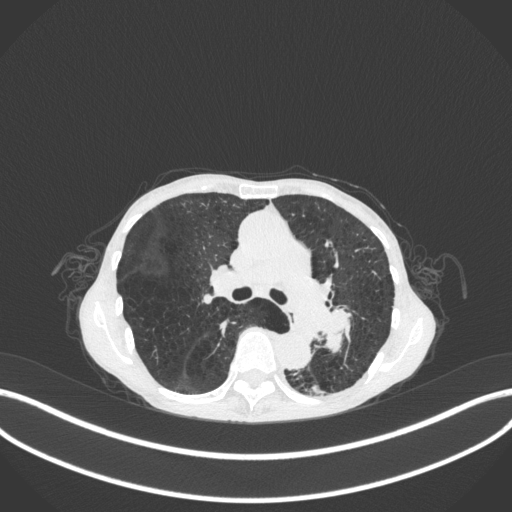
Chest CT, one axial slice; position 172 of 347 along the scan axis; reconstruction kernel B31f; lung window (W 1500 / L -600 HU); 1 mm slice thickness; 512 × 512 image matrix, field of view 400 × 400 mm. Female patient, age 70 years. From the clinical record (not read from this slice): clinical TNM (as recorded): T3 N0 M0; histopathological grade: G3.
Annotated regions visible in this slice (bounding box drawn by a radiologist):
- lung tumour (recorded histology: small cell carcinoma): bounding box <311,293,357,361> (left, top, right, bottom; pixels)